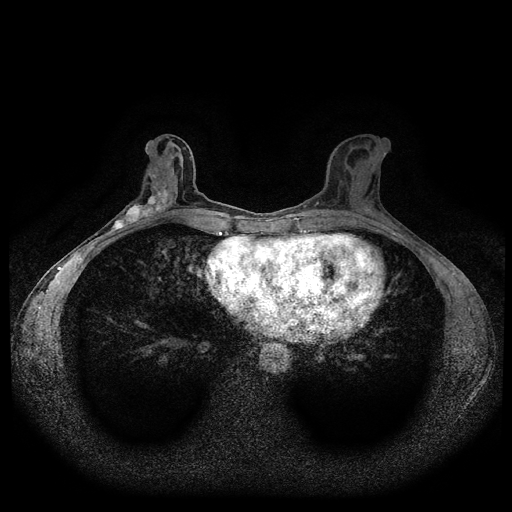
Breast MRI (dynamic contrast-enhanced, multi-phase), one axial slice. Slice 47 of 116 in the series (ordered by position). Dynamic contrast-enhanced series, time point 2 of 5 at this slice position (early post-contrast). 1.5 T. TE 2.6 ms, TR 5.3 ms. 512 × 512 image matrix, field of view 350 × 350 mm. Female patient, age 50 years.
Annotated regions visible in this slice (semi-automatic segmentation, software-assisted and operator-edited):
- breast lesion (labelled 'tumour' in the annotation; benign lesions carry a separate 'benign' label): bounding box [x1, y1, x2, y2] px = [109, 185, 174, 234]